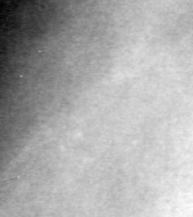
Crop from a digitized film mammogram around one marked abnormality, left breast, CC view.
Finding: calcifications, morphology pleomorphic, distribution clustered; BI-RADS assessment category 4; subtlety rating 1 on a 1 (subtle) to 5 (obvious) scale; pathology (as recorded): benign.